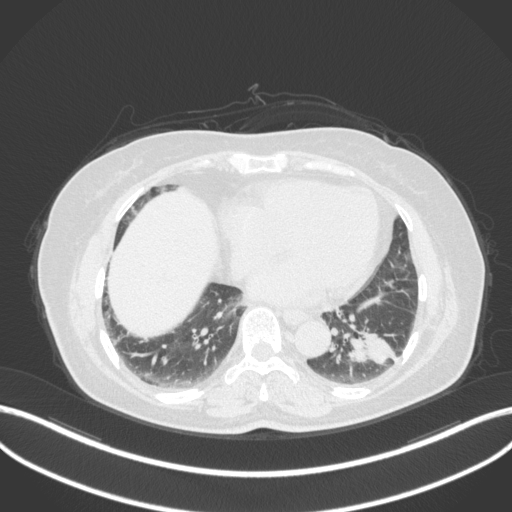
Chest CT, one axial slice; slice 134 of 307 in the series (ordered by position); reconstruction kernel B31f; 120 kVp; lung window (W 1500 / L -600 HU); 1 mm slice thickness; 512 × 512 image matrix, field of view 400 × 400 mm. Patient: female, 59 years. From the clinical record (not read from this slice): clinical TNM (as recorded): T2a N0 M0; histopathological grade: G2-3.
Outlined on this slice (bounding box drawn by a radiologist):
- lung tumour (recorded histology: adenocarcinoma): bounding box <344,323,402,370> (left, top, right, bottom; pixels)